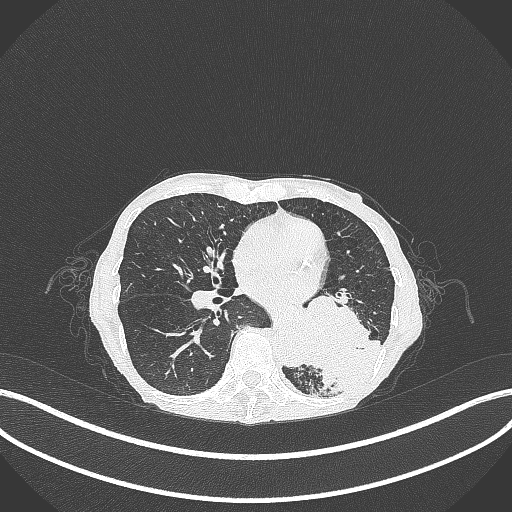
Chest CT, one axial slice; slice 124 of 347 in the series (ordered by position); reconstruction kernel B70f; lung window (W 1500 / L -600 HU); 512 × 512 image matrix, field of view 400 × 400 mm. Female patient, age 70 years. Case-level facts recorded for this patient, not image findings: clinical TNM (as recorded): T3 N0 M0.
Annotated regions visible in this slice (bounding box drawn by a radiologist):
- lung tumour (recorded histology: small cell carcinoma): bounding box [x1, y1, x2, y2] px = [293, 286, 382, 391]